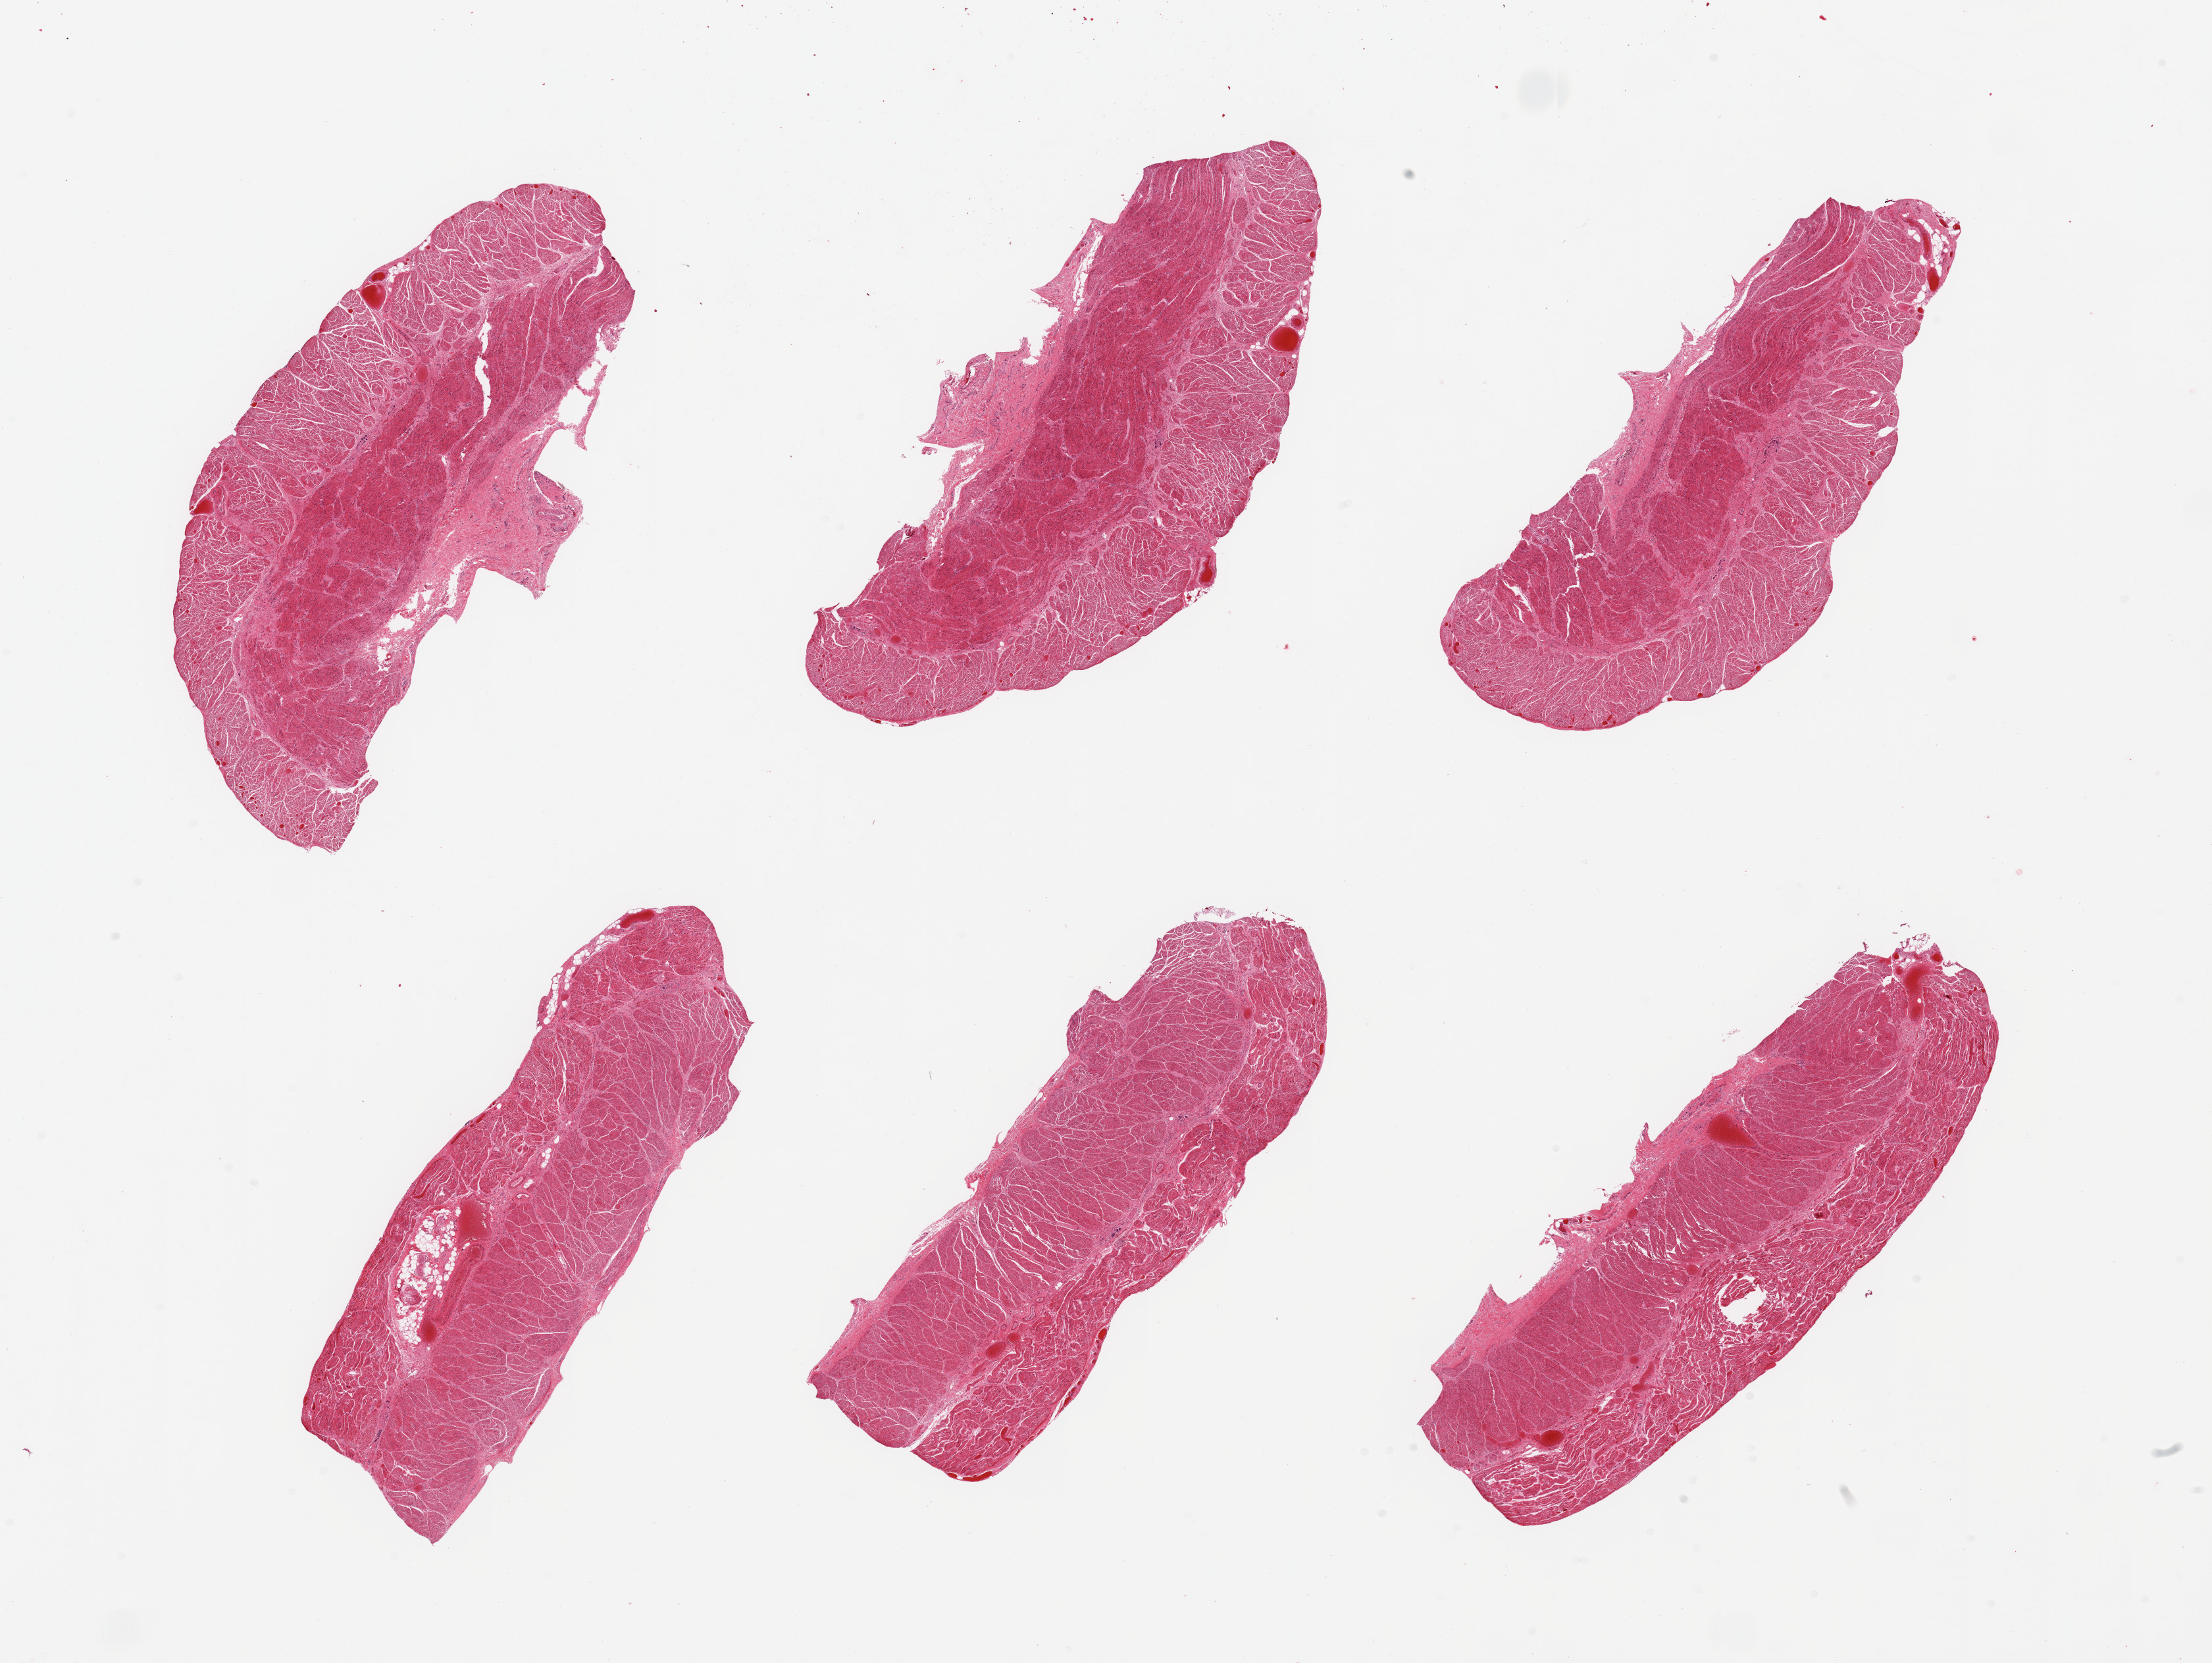
Whole-slide image, hematoxylin and eosin (H&E) stain, shown as a low-resolution overview of the whole scanned area (about 26.6 x 20.0 mm). PAXgene-fixed, paraffin-embedded tissue. Section of gastroesophageal junction (target tissue). Tissue donor sample. Male donor.
Review note (as recorded): 6 pieces; target muscularis.